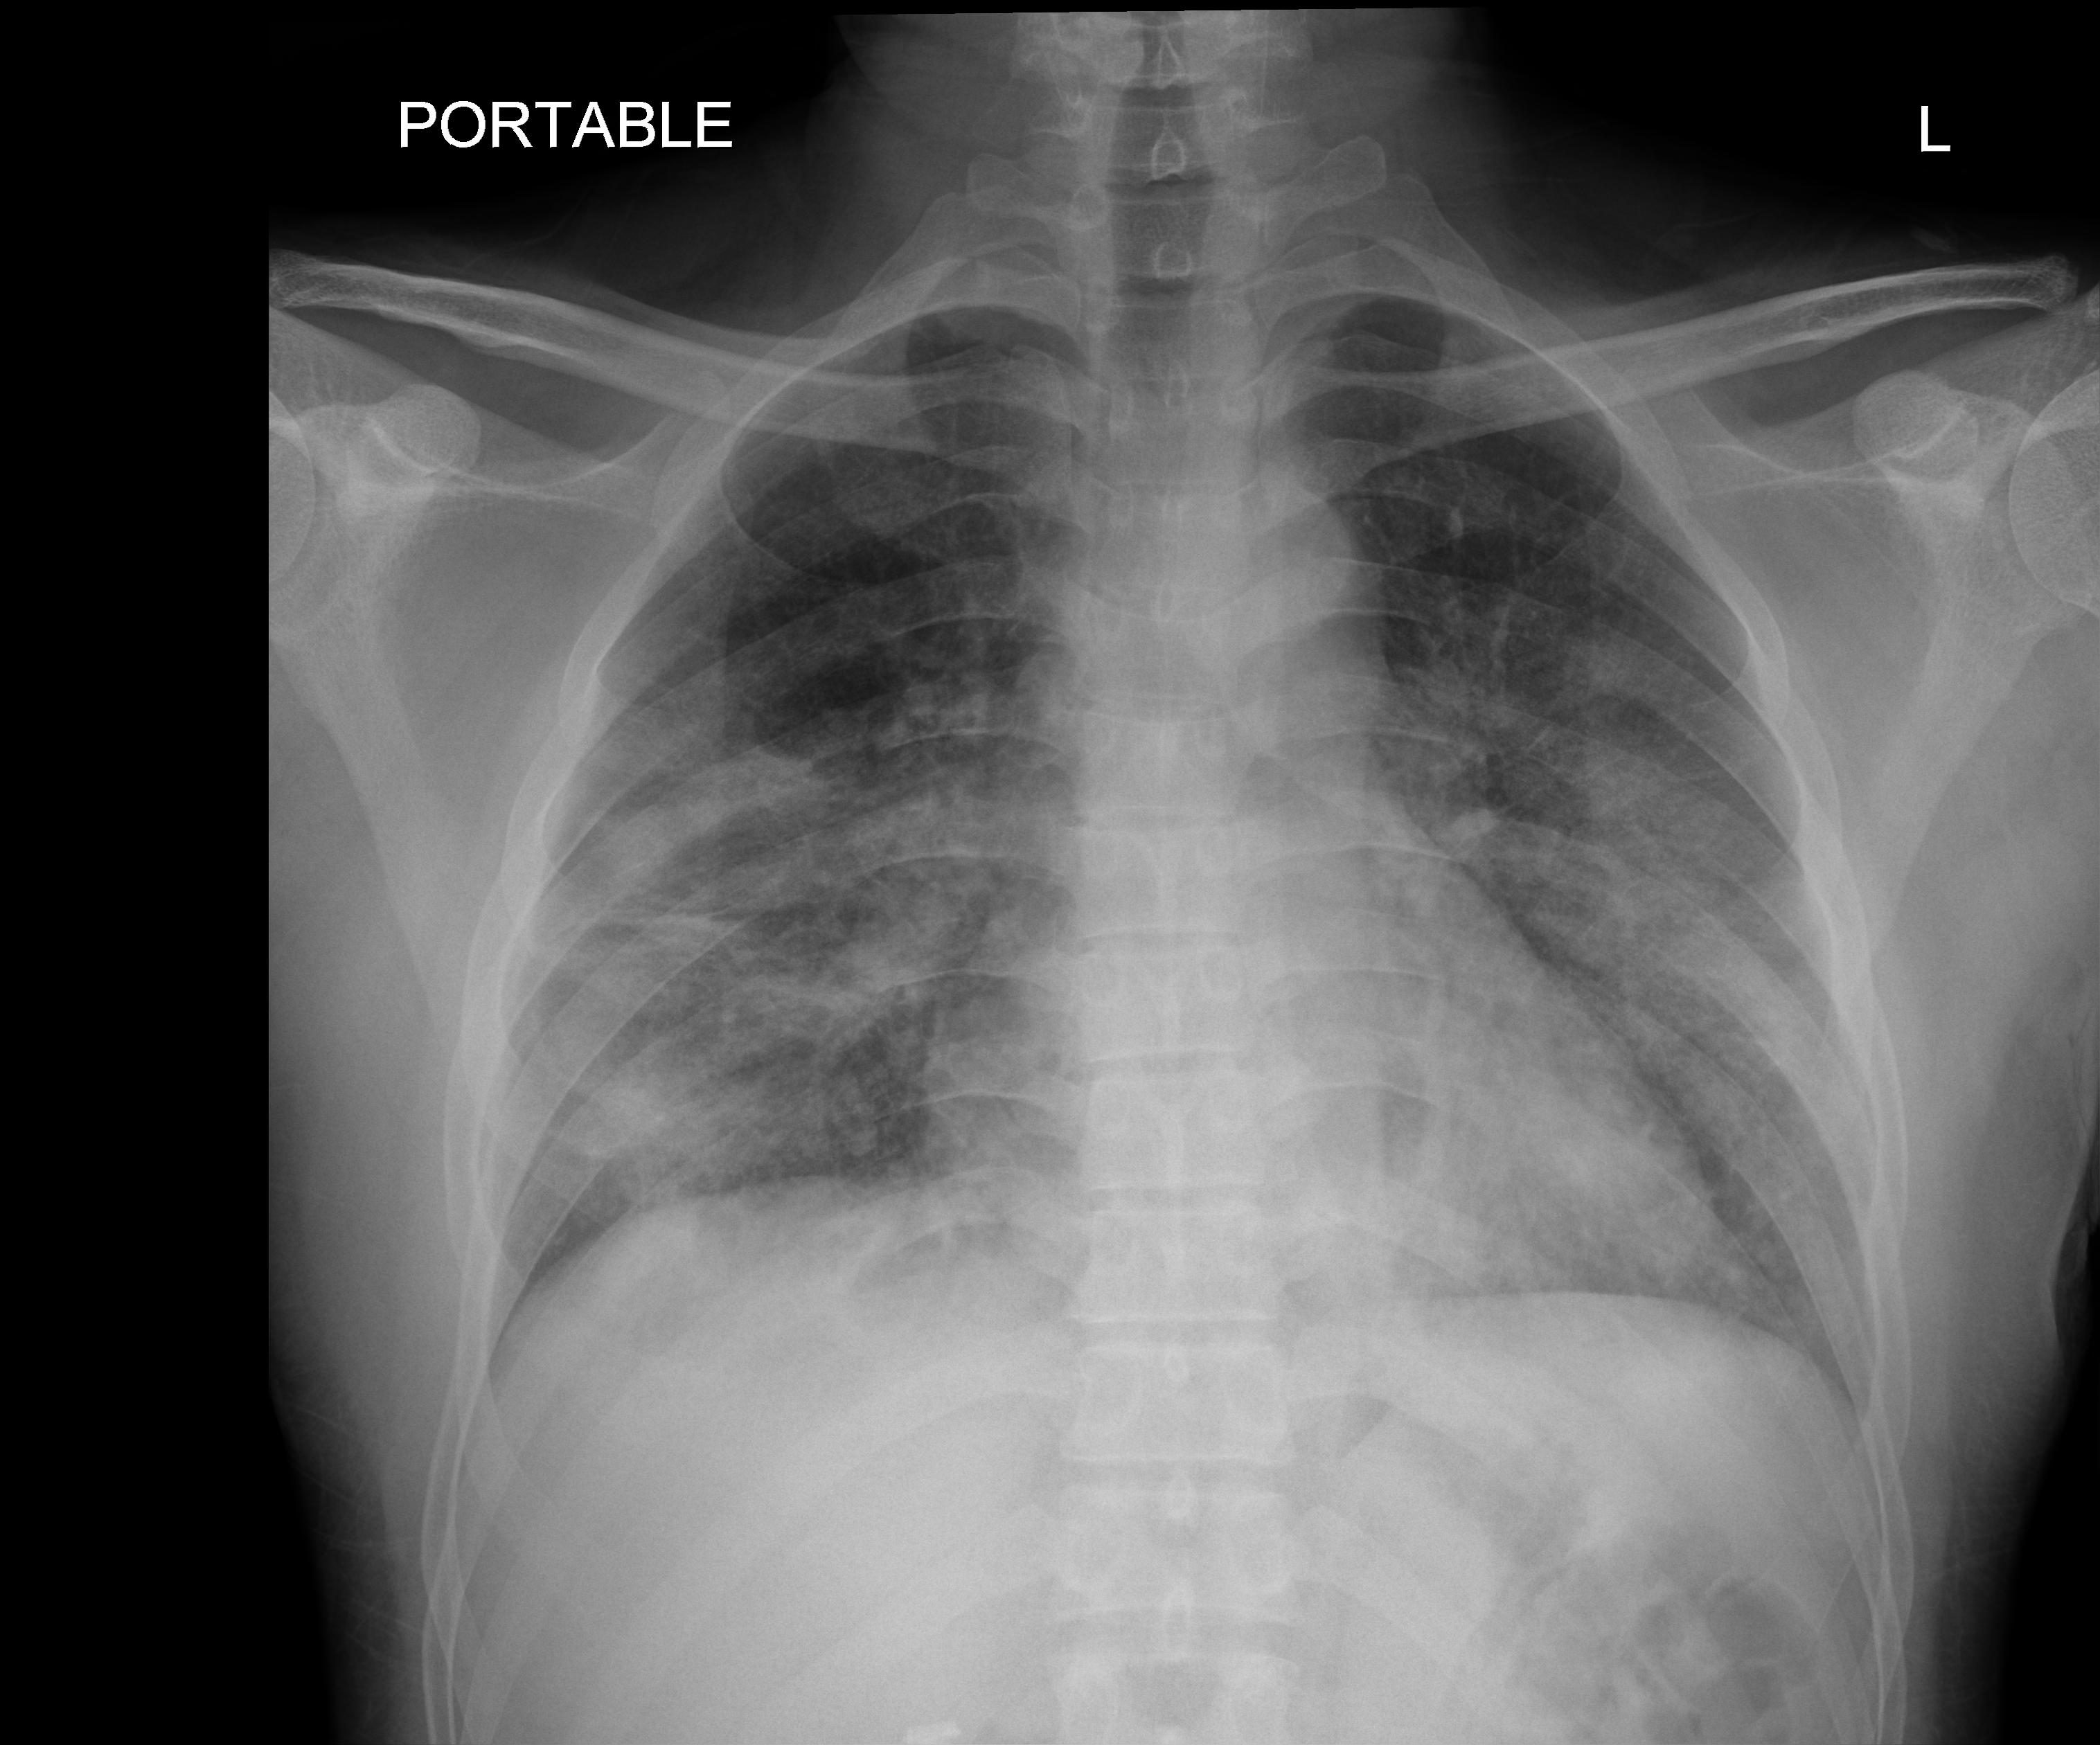
Chest radiograph. Patient hospitalised with COVID-19; male, aged 18–59 years.
From the hospital-stay record, not from the radiograph (when in the stay this image was taken is not recorded): hypertension (admission record): no; smoking status (admission record): never; mechanically ventilated during this hospital stay: no.